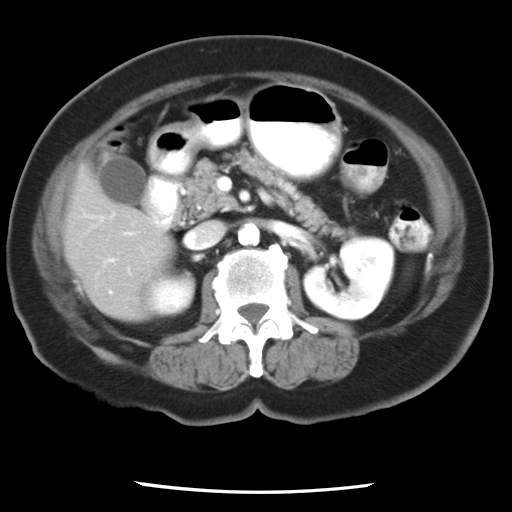
Contrast-enhanced abdominal CT, one axial slice. Slice 9 of 24 in the series (ordered by position). Intravenous contrast given. Soft-tissue window (W 400 / L 40 HU). 512 × 512 image matrix, field of view 312 × 312 mm. Female patient, age 71 years. Case-level facts recorded for this patient, not image findings: diagnosis: colorectal cancer liver metastases, imaged before liver resection; multiple liver metastases: no; largest metastasis: 4.3 cm; disease in both lobes: no.
Structures marked on this image (outlined manually by an expert reader):
- hepatic veins: bounding box (x1, y1, x2, y2) in pixels: (109, 292, 111, 294)
- liver: (64, 166, 172, 317)
- planned liver remnant (the part of the liver to remain after resection): (65, 166, 172, 317)
- portal vein (with intrahepatic branches): (104, 257, 115, 263)